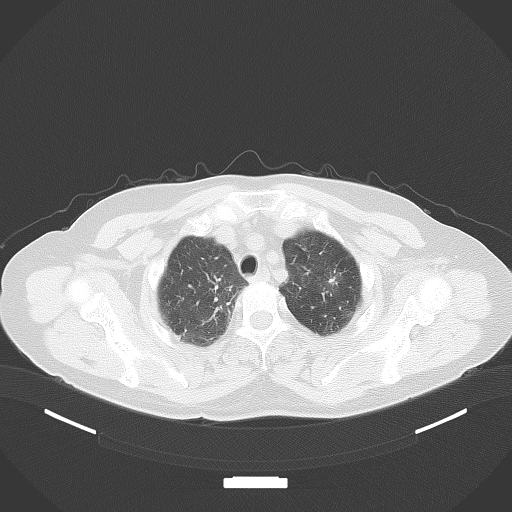
Chest CT, one axial slice; position 72 of 116 along the scan axis; lung window (W 1500 / L -600 HU); 512 × 512 image matrix. Patient: female, 64 years. From the clinical record (not read from this slice): clinical TNM (as recorded): T1c N0 M0; histopathological grade: G1.
Outlined on this slice (rectangle marked by the reading radiologist):
- lung tumour (recorded histology: adenocarcinoma): bounding box (x1, y1, x2, y2) in pixels: (325, 268, 342, 295)